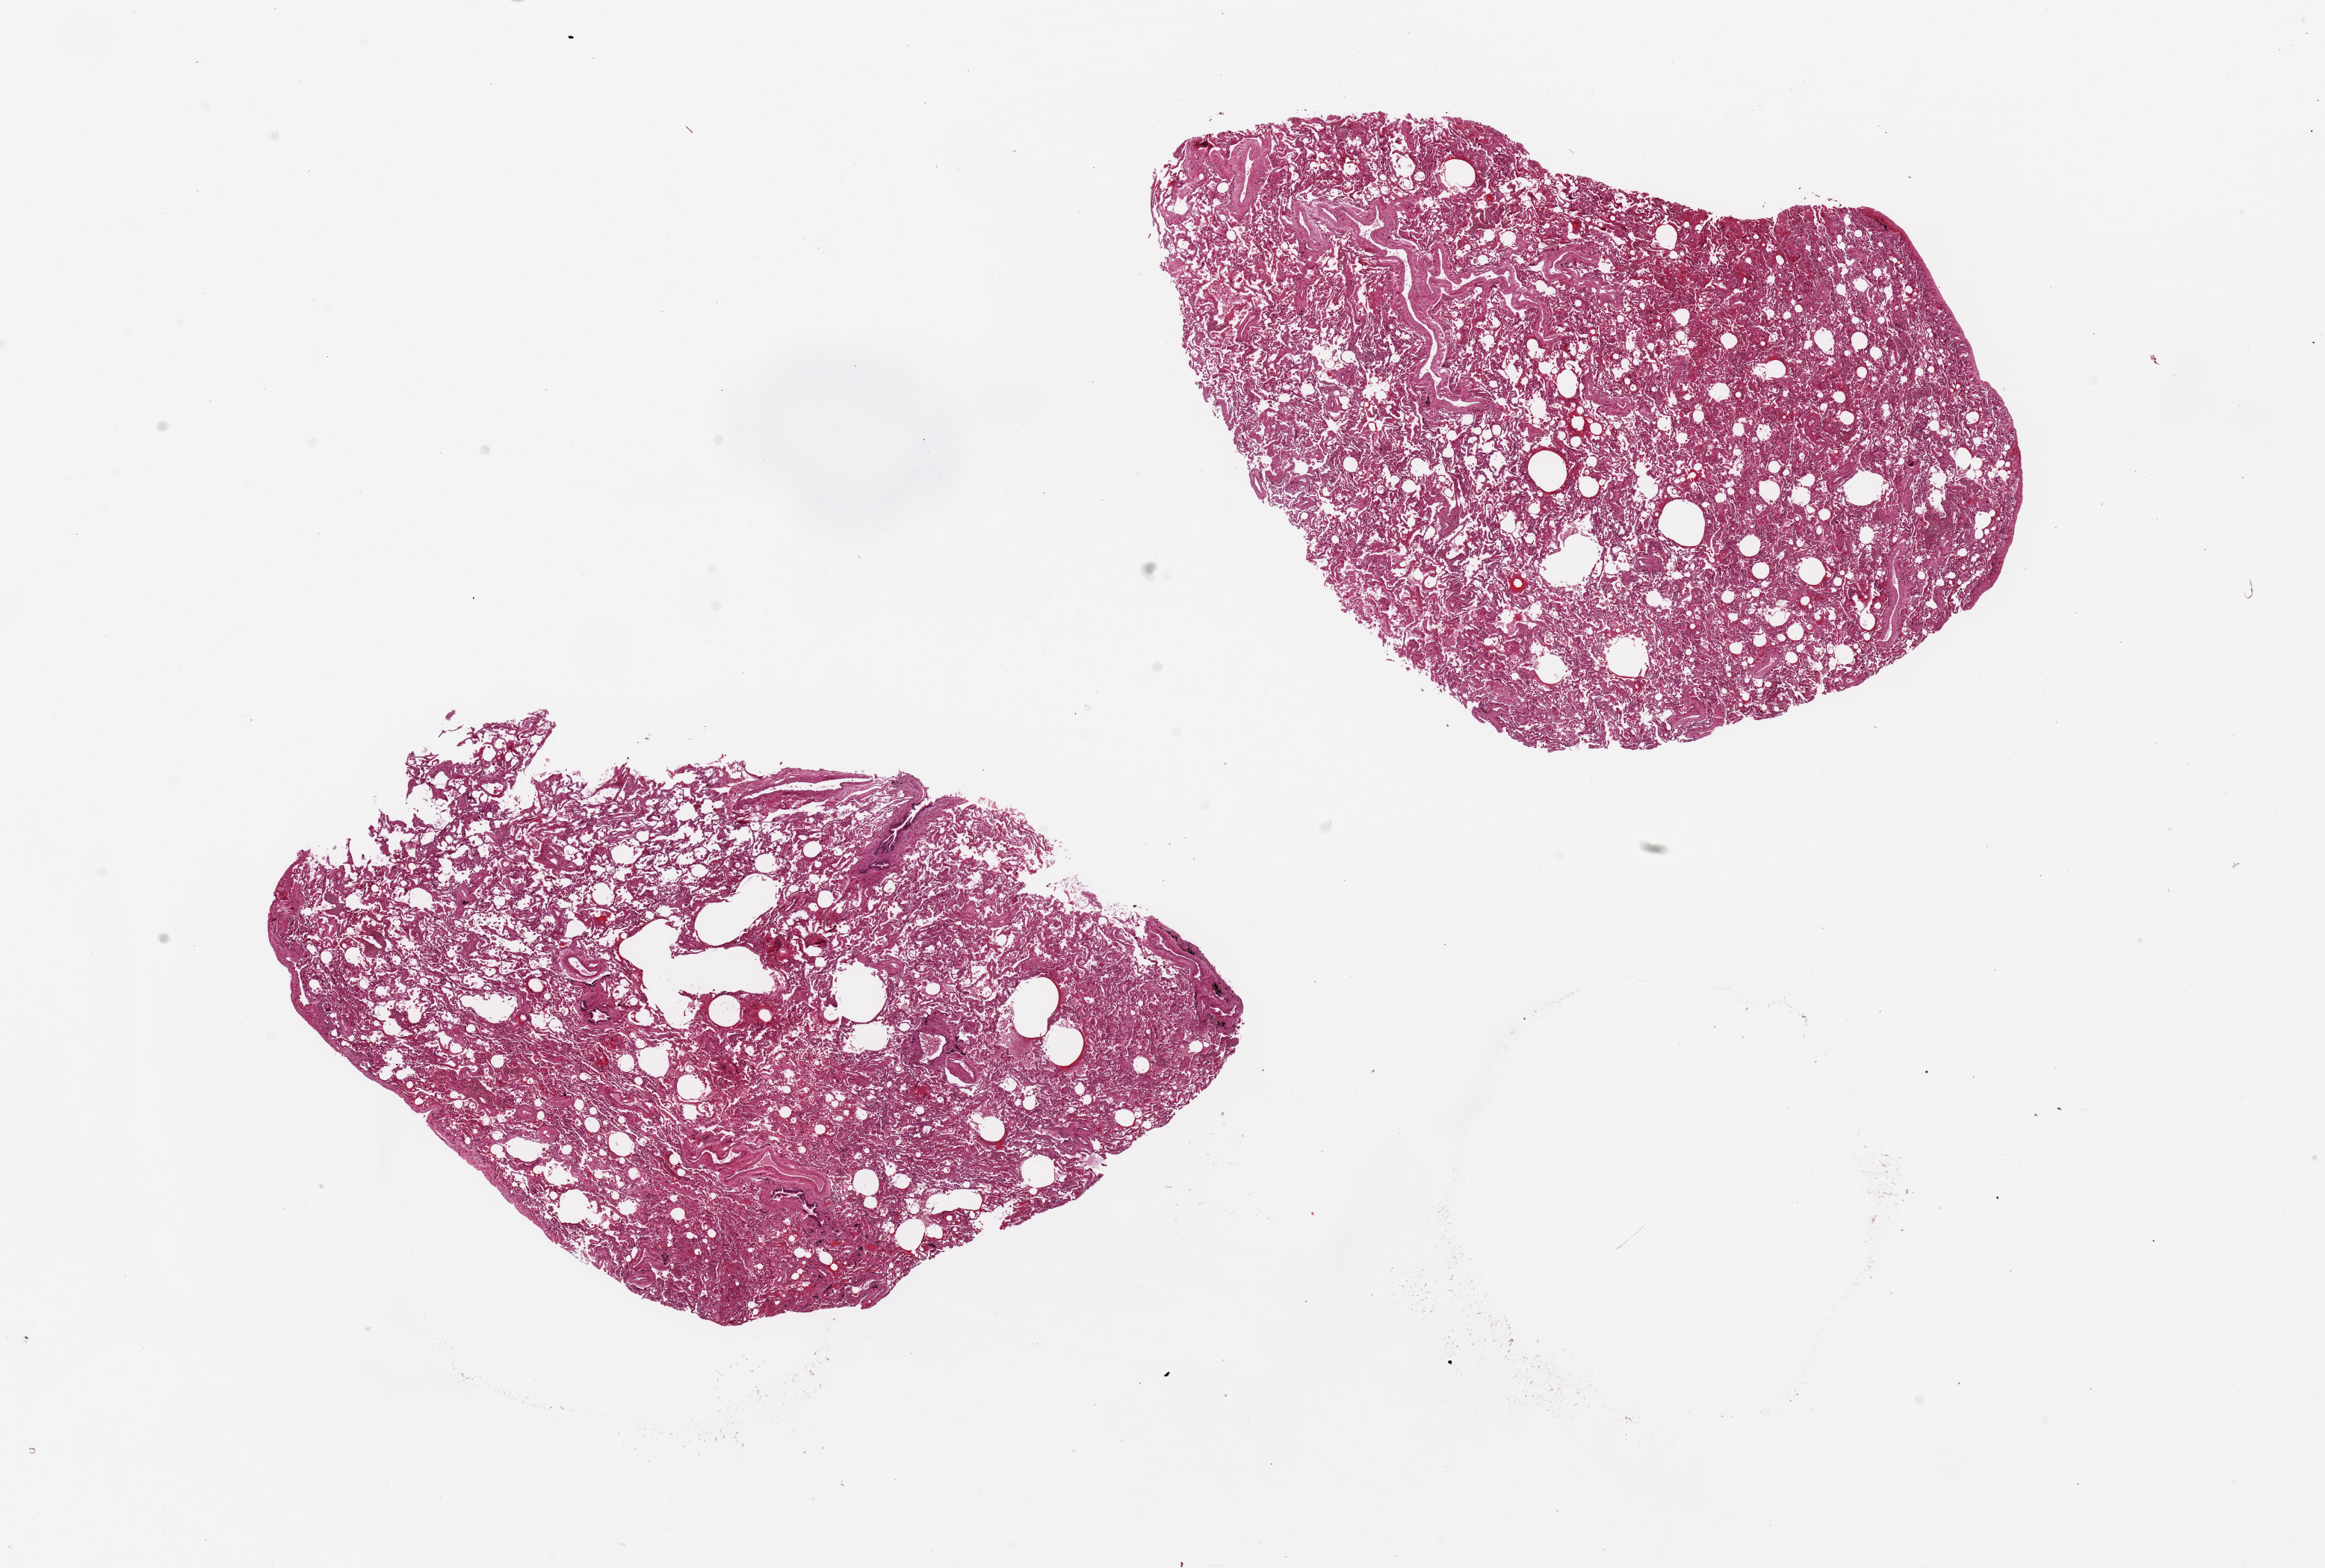
Whole-slide image, H&E stain — a low-resolution overview of the entire scanned area, about 24.6 x 16.6 mm (from a 20x scan); PAXgene-fixed, paraffin-embedded tissue; sampled site (target tissue): lung; tissue donor sample. Female donor.
Review note (as recorded): 2 pieces, 8x7 & 9x7mm.